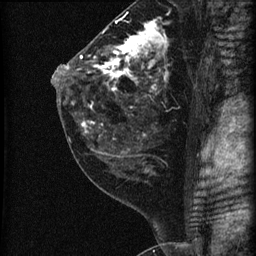
Breast MRI (dynamic contrast-enhanced), one sagittal slice. Slice 34 of 60 in the series (ordered by position). Dynamic contrast-enhanced series, image 2 of 3 at this slice position (ordered by acquisition). 1.5 T. TE 4.2 ms, TR 22.7 ms. 1.8 mm slice thickness. 256 × 256 image matrix, field of view 180 × 180 mm. Female patient, age 45 years. From the clinical record (not read from this slice): setting: breast cancer imaged before/during neoadjuvant chemotherapy; receptor status: HR-positive, HER2-negative.
Structures marked on this image (semi-automatically segmented with operator editing):
- analysis volume of interest (the breast-tissue region the enhancement analysis was run in; not a lesion): box from (x=74, y=11) to (x=205, y=140) px
- tumour enhancement mask (voxels above the 90 % enhancement threshold inside the analysis volume of interest): (x=80, y=21)–(x=168, y=133)